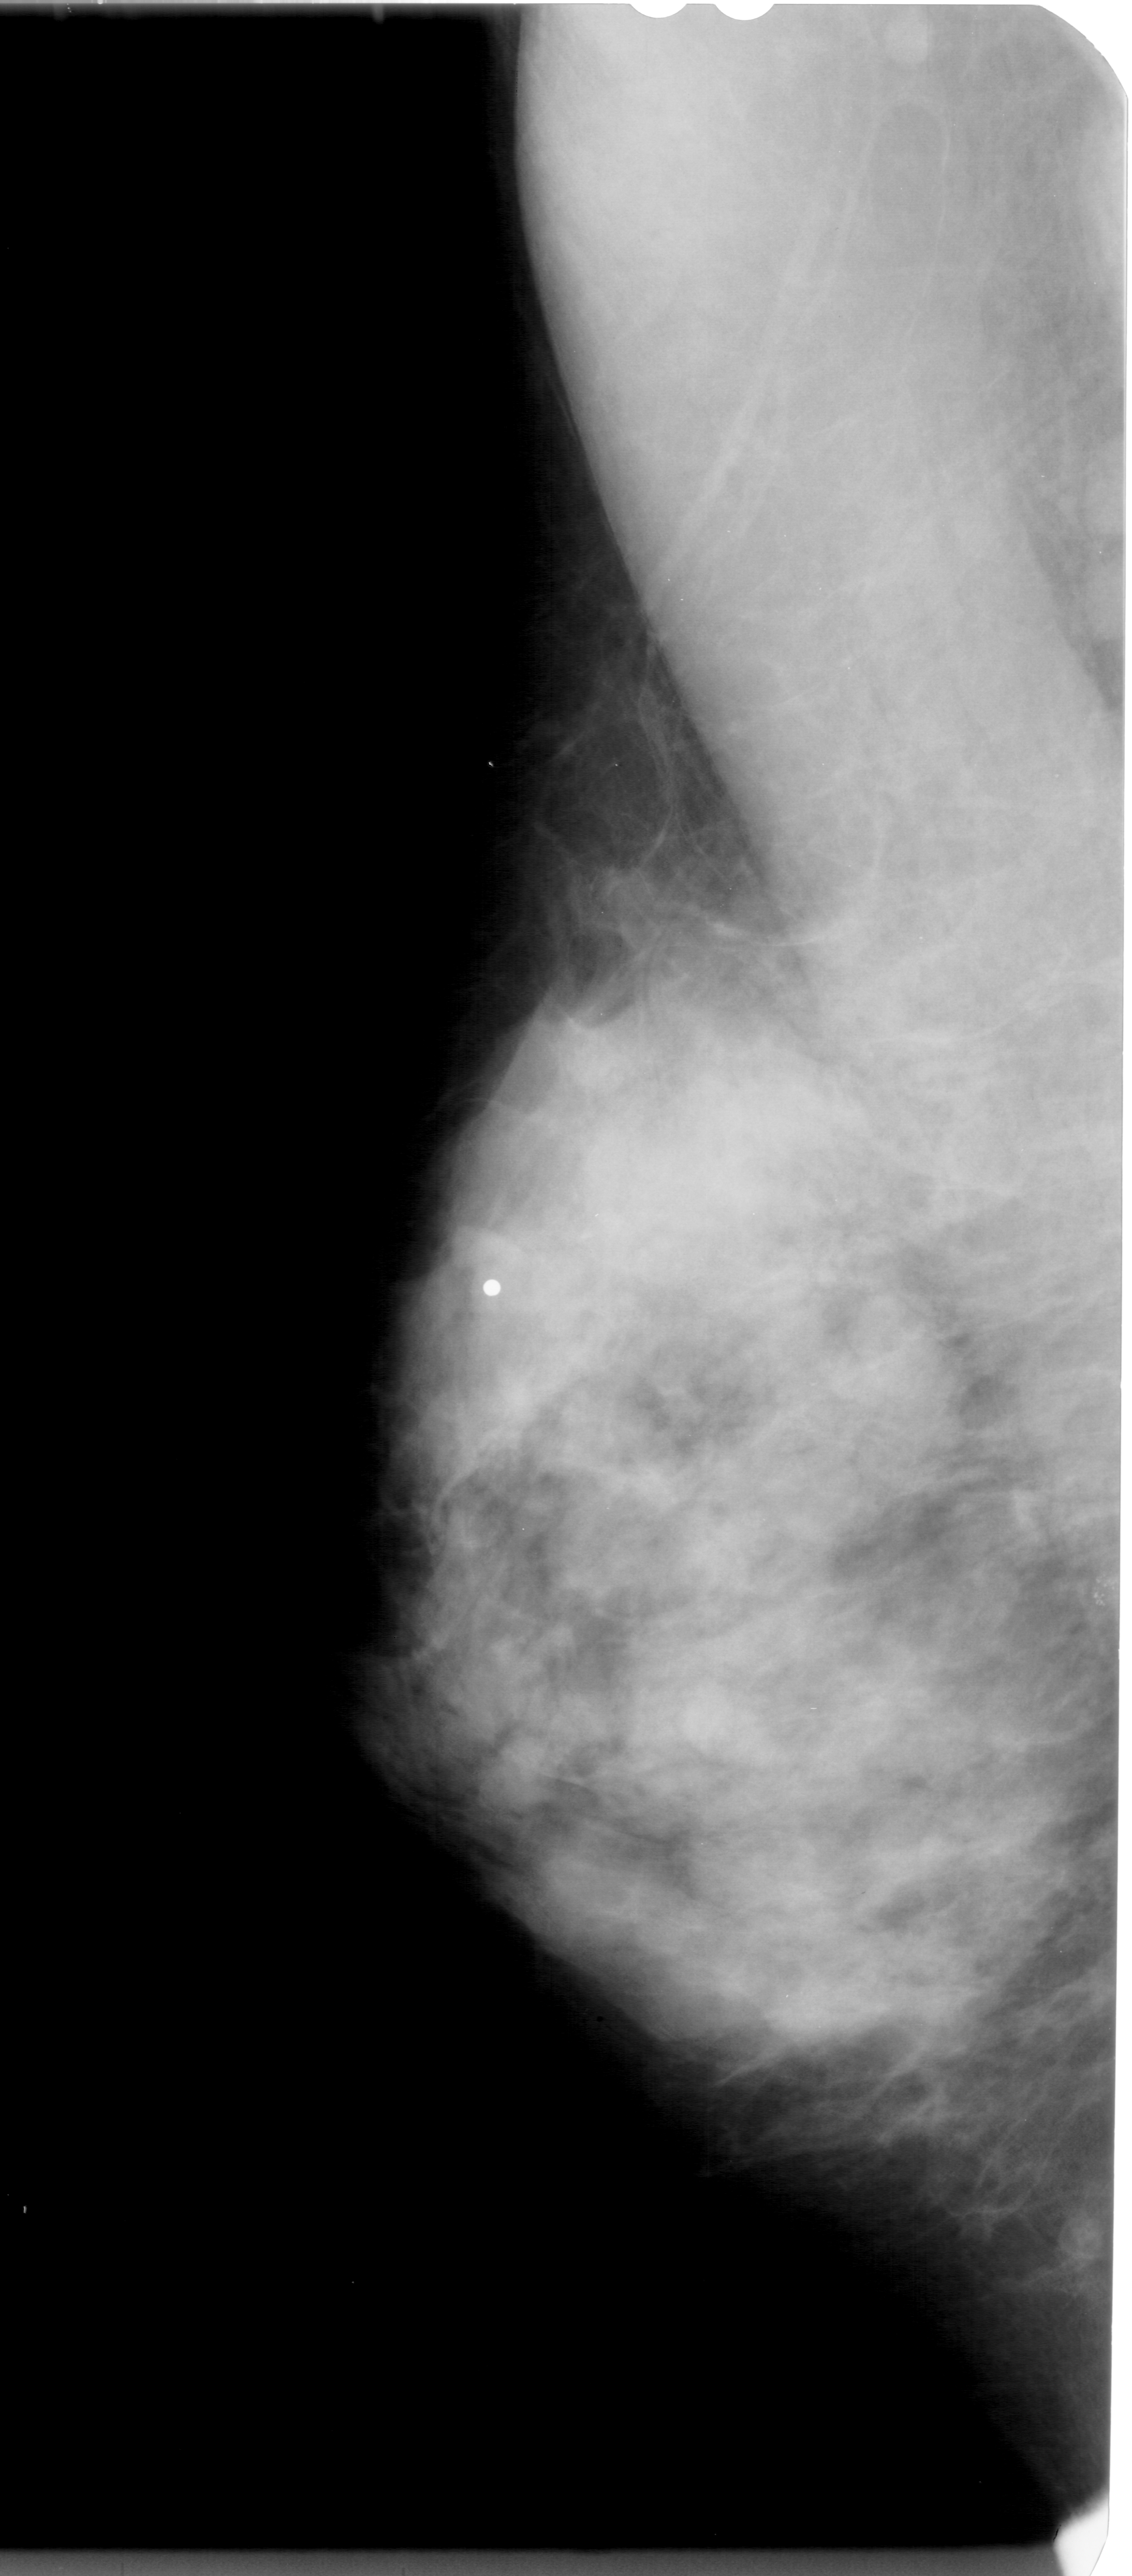
Scanned film-screen mammogram; left breast; MLO view; BI-RADS breast density category 4 (scale 1–4).
- Radiologist-marked abnormalities on this image: calcifications, morphology pleomorphic, distribution clustered; BI-RADS assessment category 4; pathology (as recorded): benign.